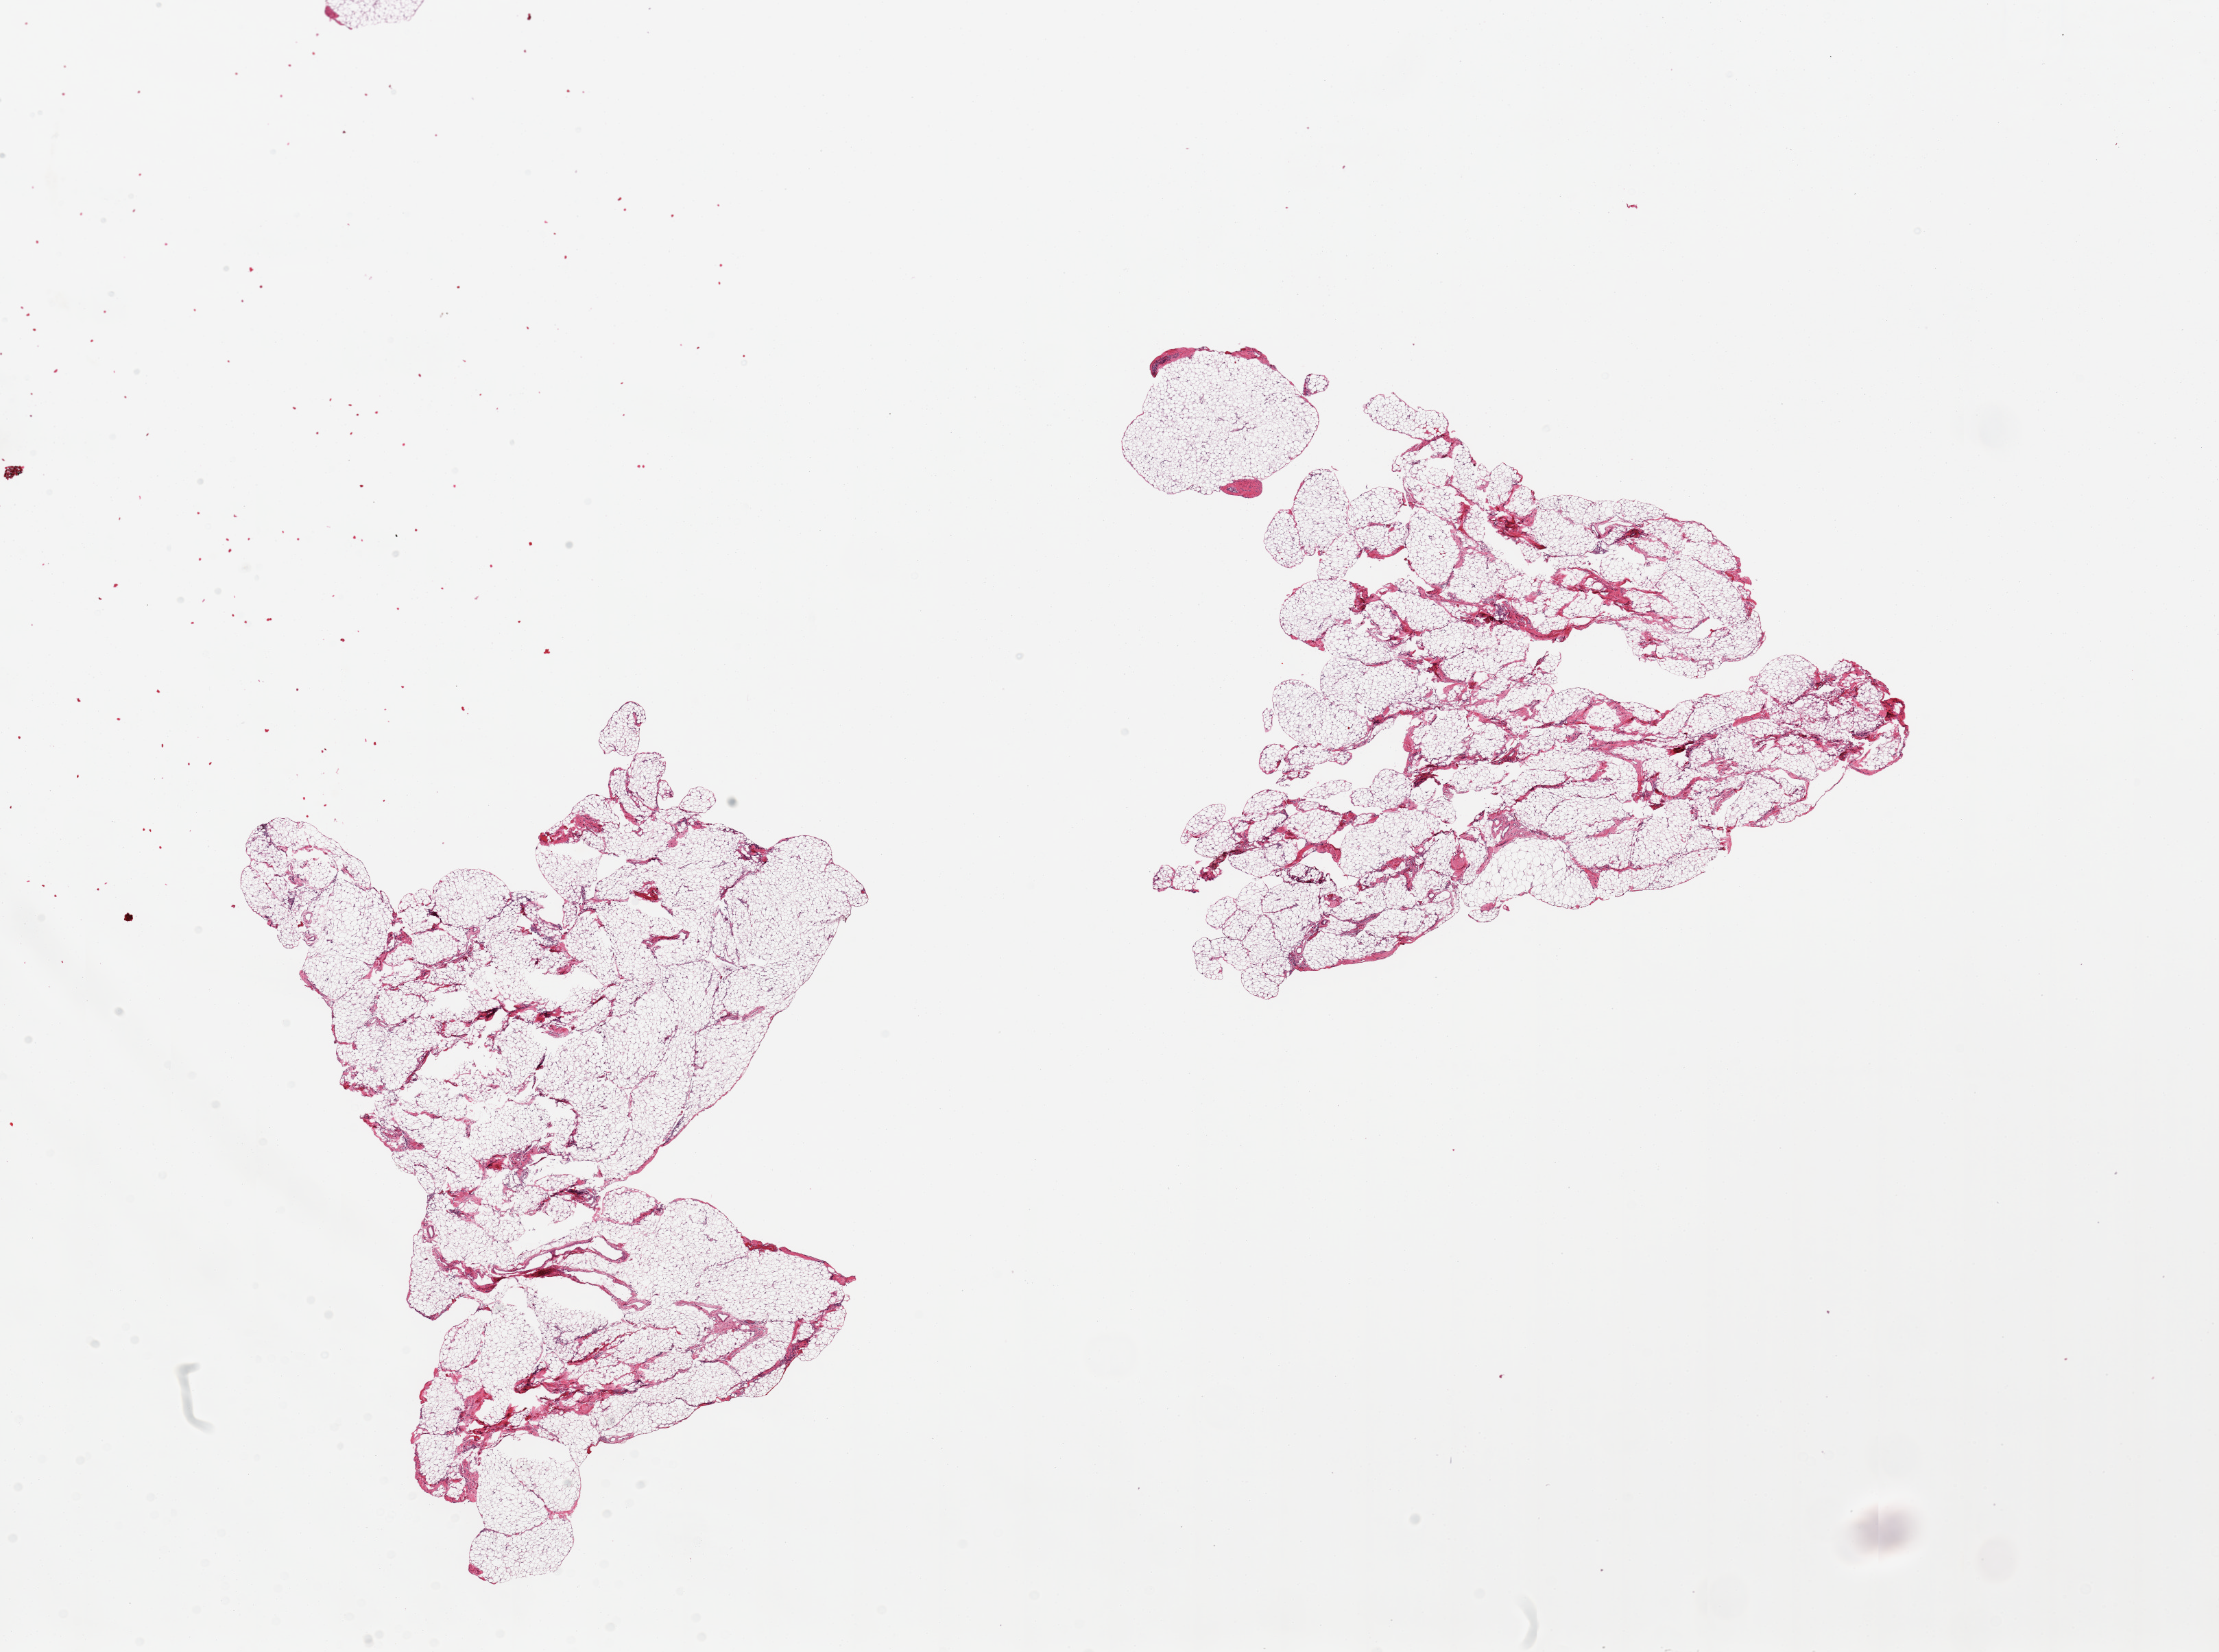
Whole-slide image, haematoxylin and eosin stain, brightfield, shown as a low-resolution overview of the whole scanned area (about 25.6 x 19.1 mm); PAXgene-fixed paraffin-embedded (PFPE) section; target tissue: omentum; tissue donor sample. Donor sex: male.
* pathologist's review note for this sample: 2 pieces, prominent fascia/vascular elements are ~10-15% tissue